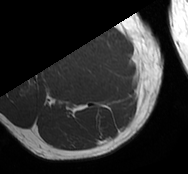
MRI of an extremity soft-tissue mass, one axial slice; MR volume resampled by the dataset authors to the PET/CT grid (not the native acquisition matrix); 188 × 174 image matrix. Male patient. From the clinical record (not read from this slice): histological type: undifferentiated - pleiomorphic; grade: high; site of the primary tumour: right thigh.
Structures marked on this image (expert contour drawn on MRI and transferred to this co-registered scan by the dataset authors):
- gross tumour volume including surrounding oedema: bounding box [x1, y1, x2, y2] px = [68, 55, 73, 61]